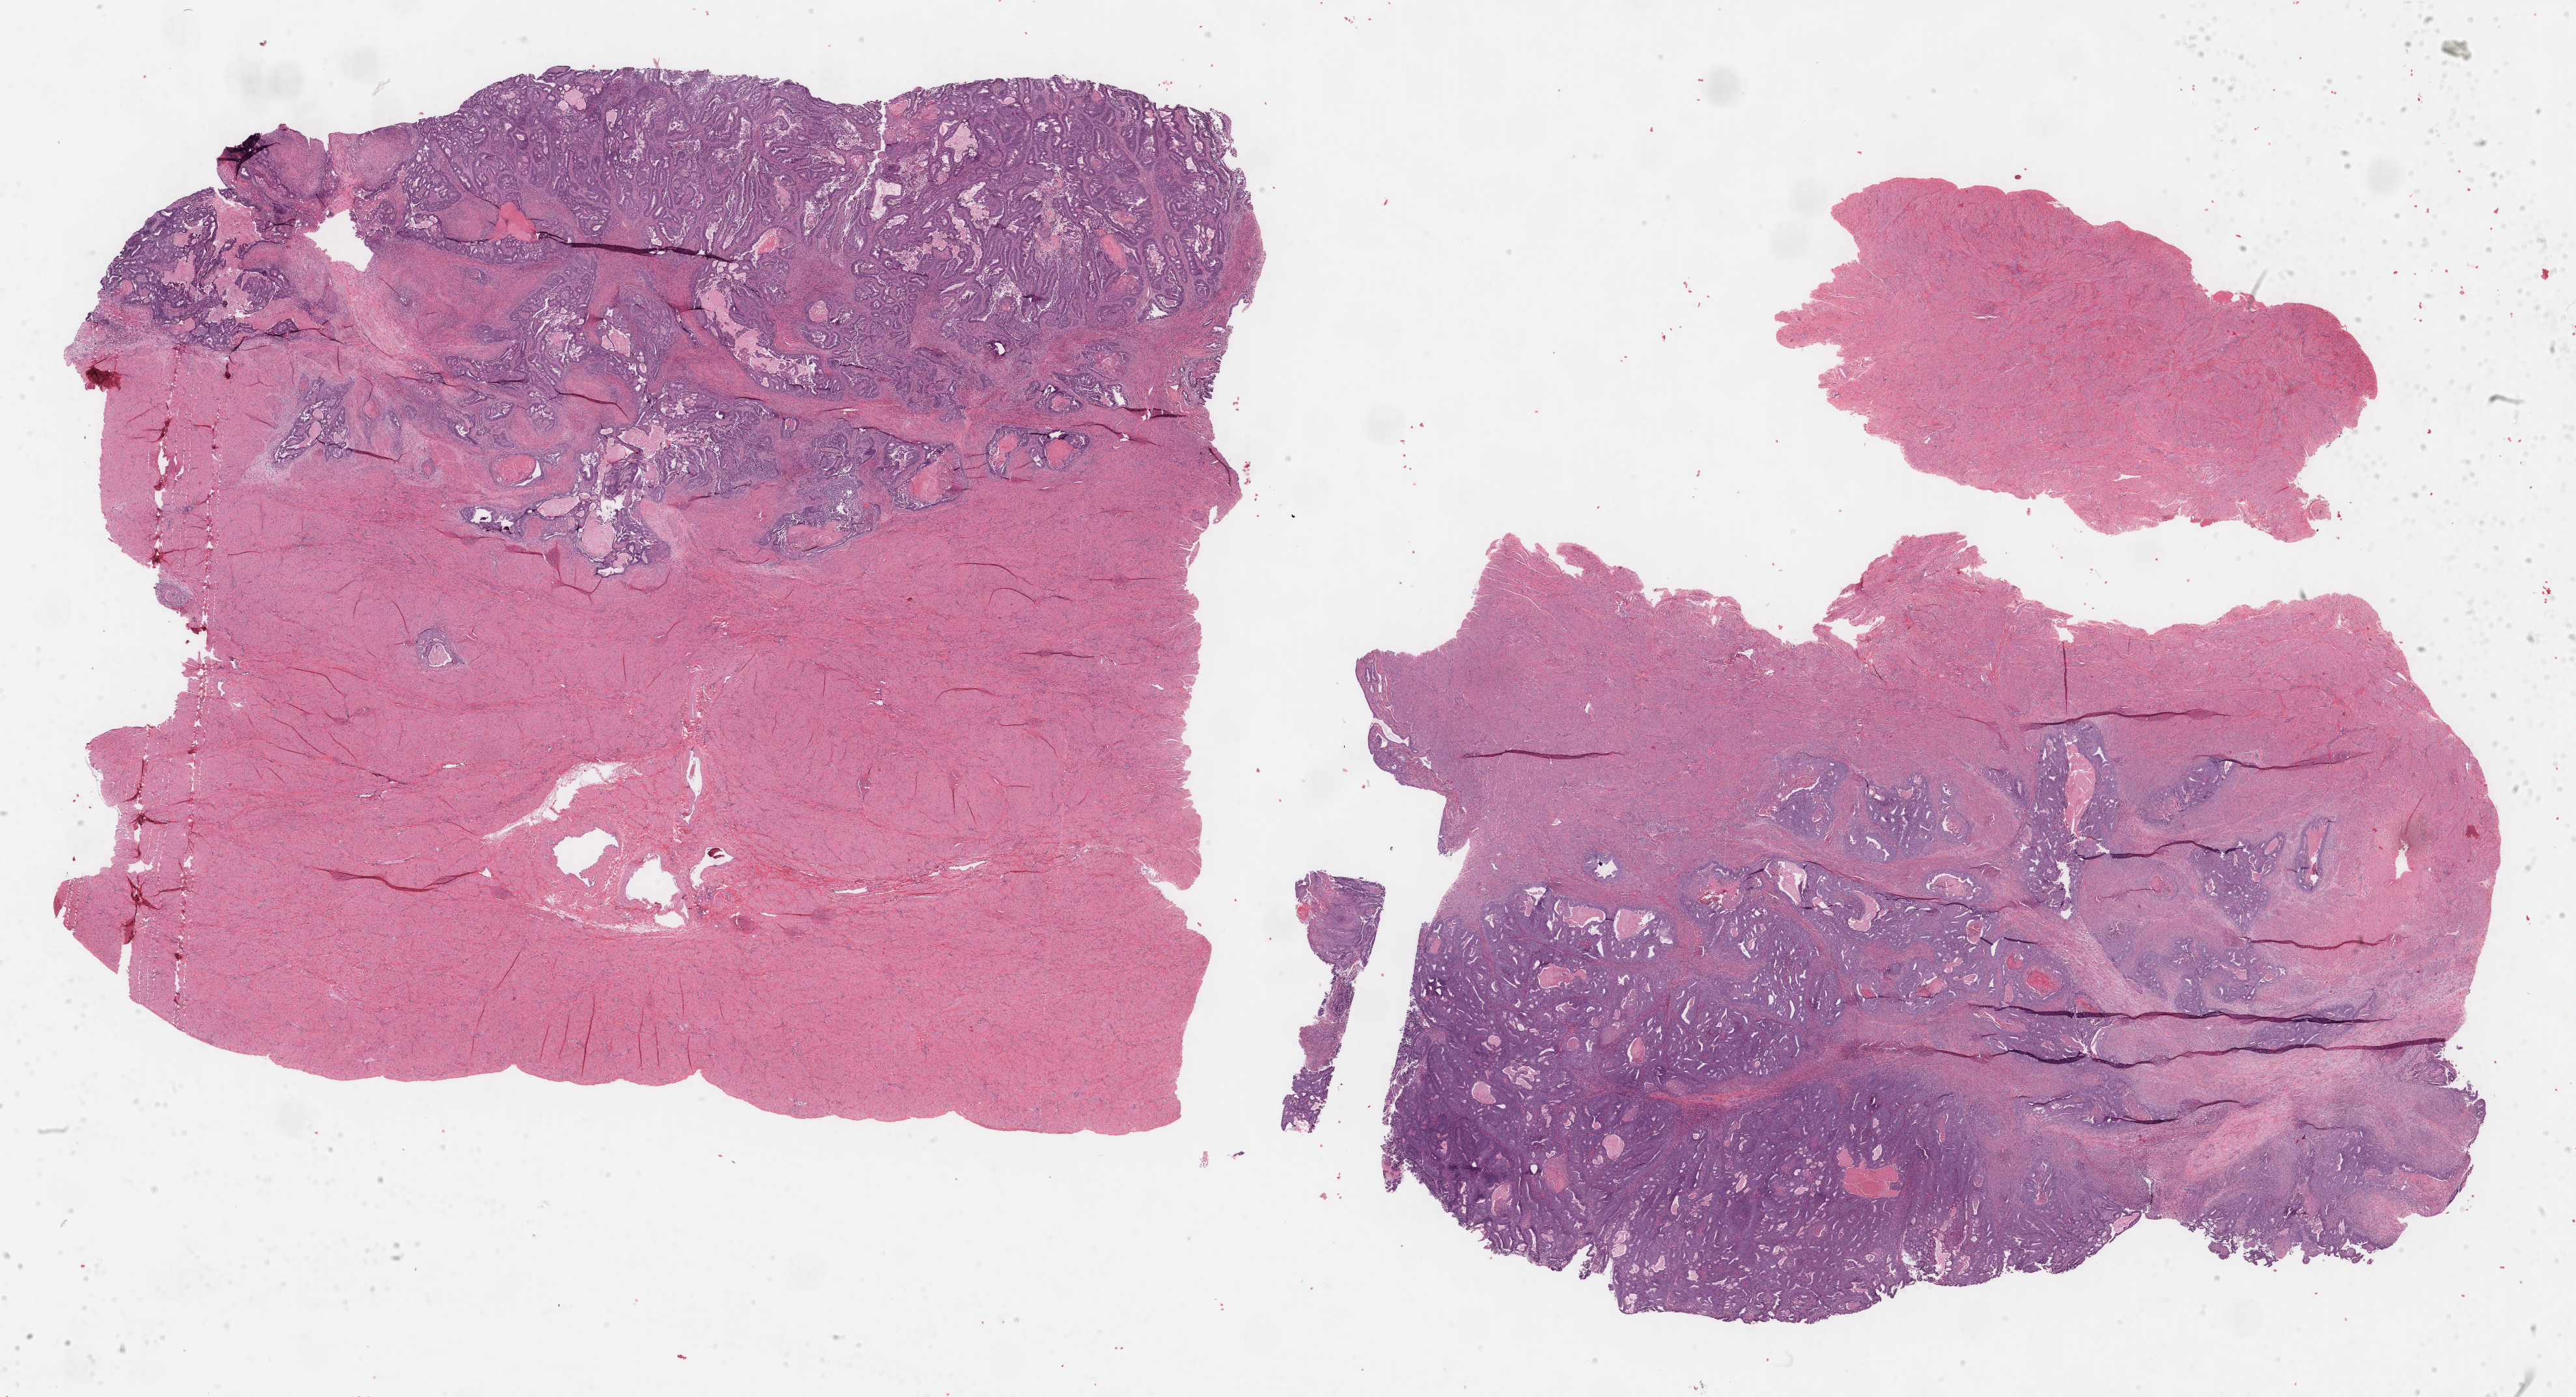
H&E whole-slide image — a low-resolution overview of the entire scanned area, about 31.4 x 17.0 mm; formalin-fixed paraffin-embedded (FFPE) diagnostic section; sample: primary tumour, uterus. Patient: female, age at initial diagnosis 49 years. Histologic grade: G2 (moderately differentiated).
Lymph nodes positive (case pathology): 0 of 34 examined. Histologic diagnosis: Endometrioid adenocarcinoma, NOS (endometrium). FIGO stage: IC.